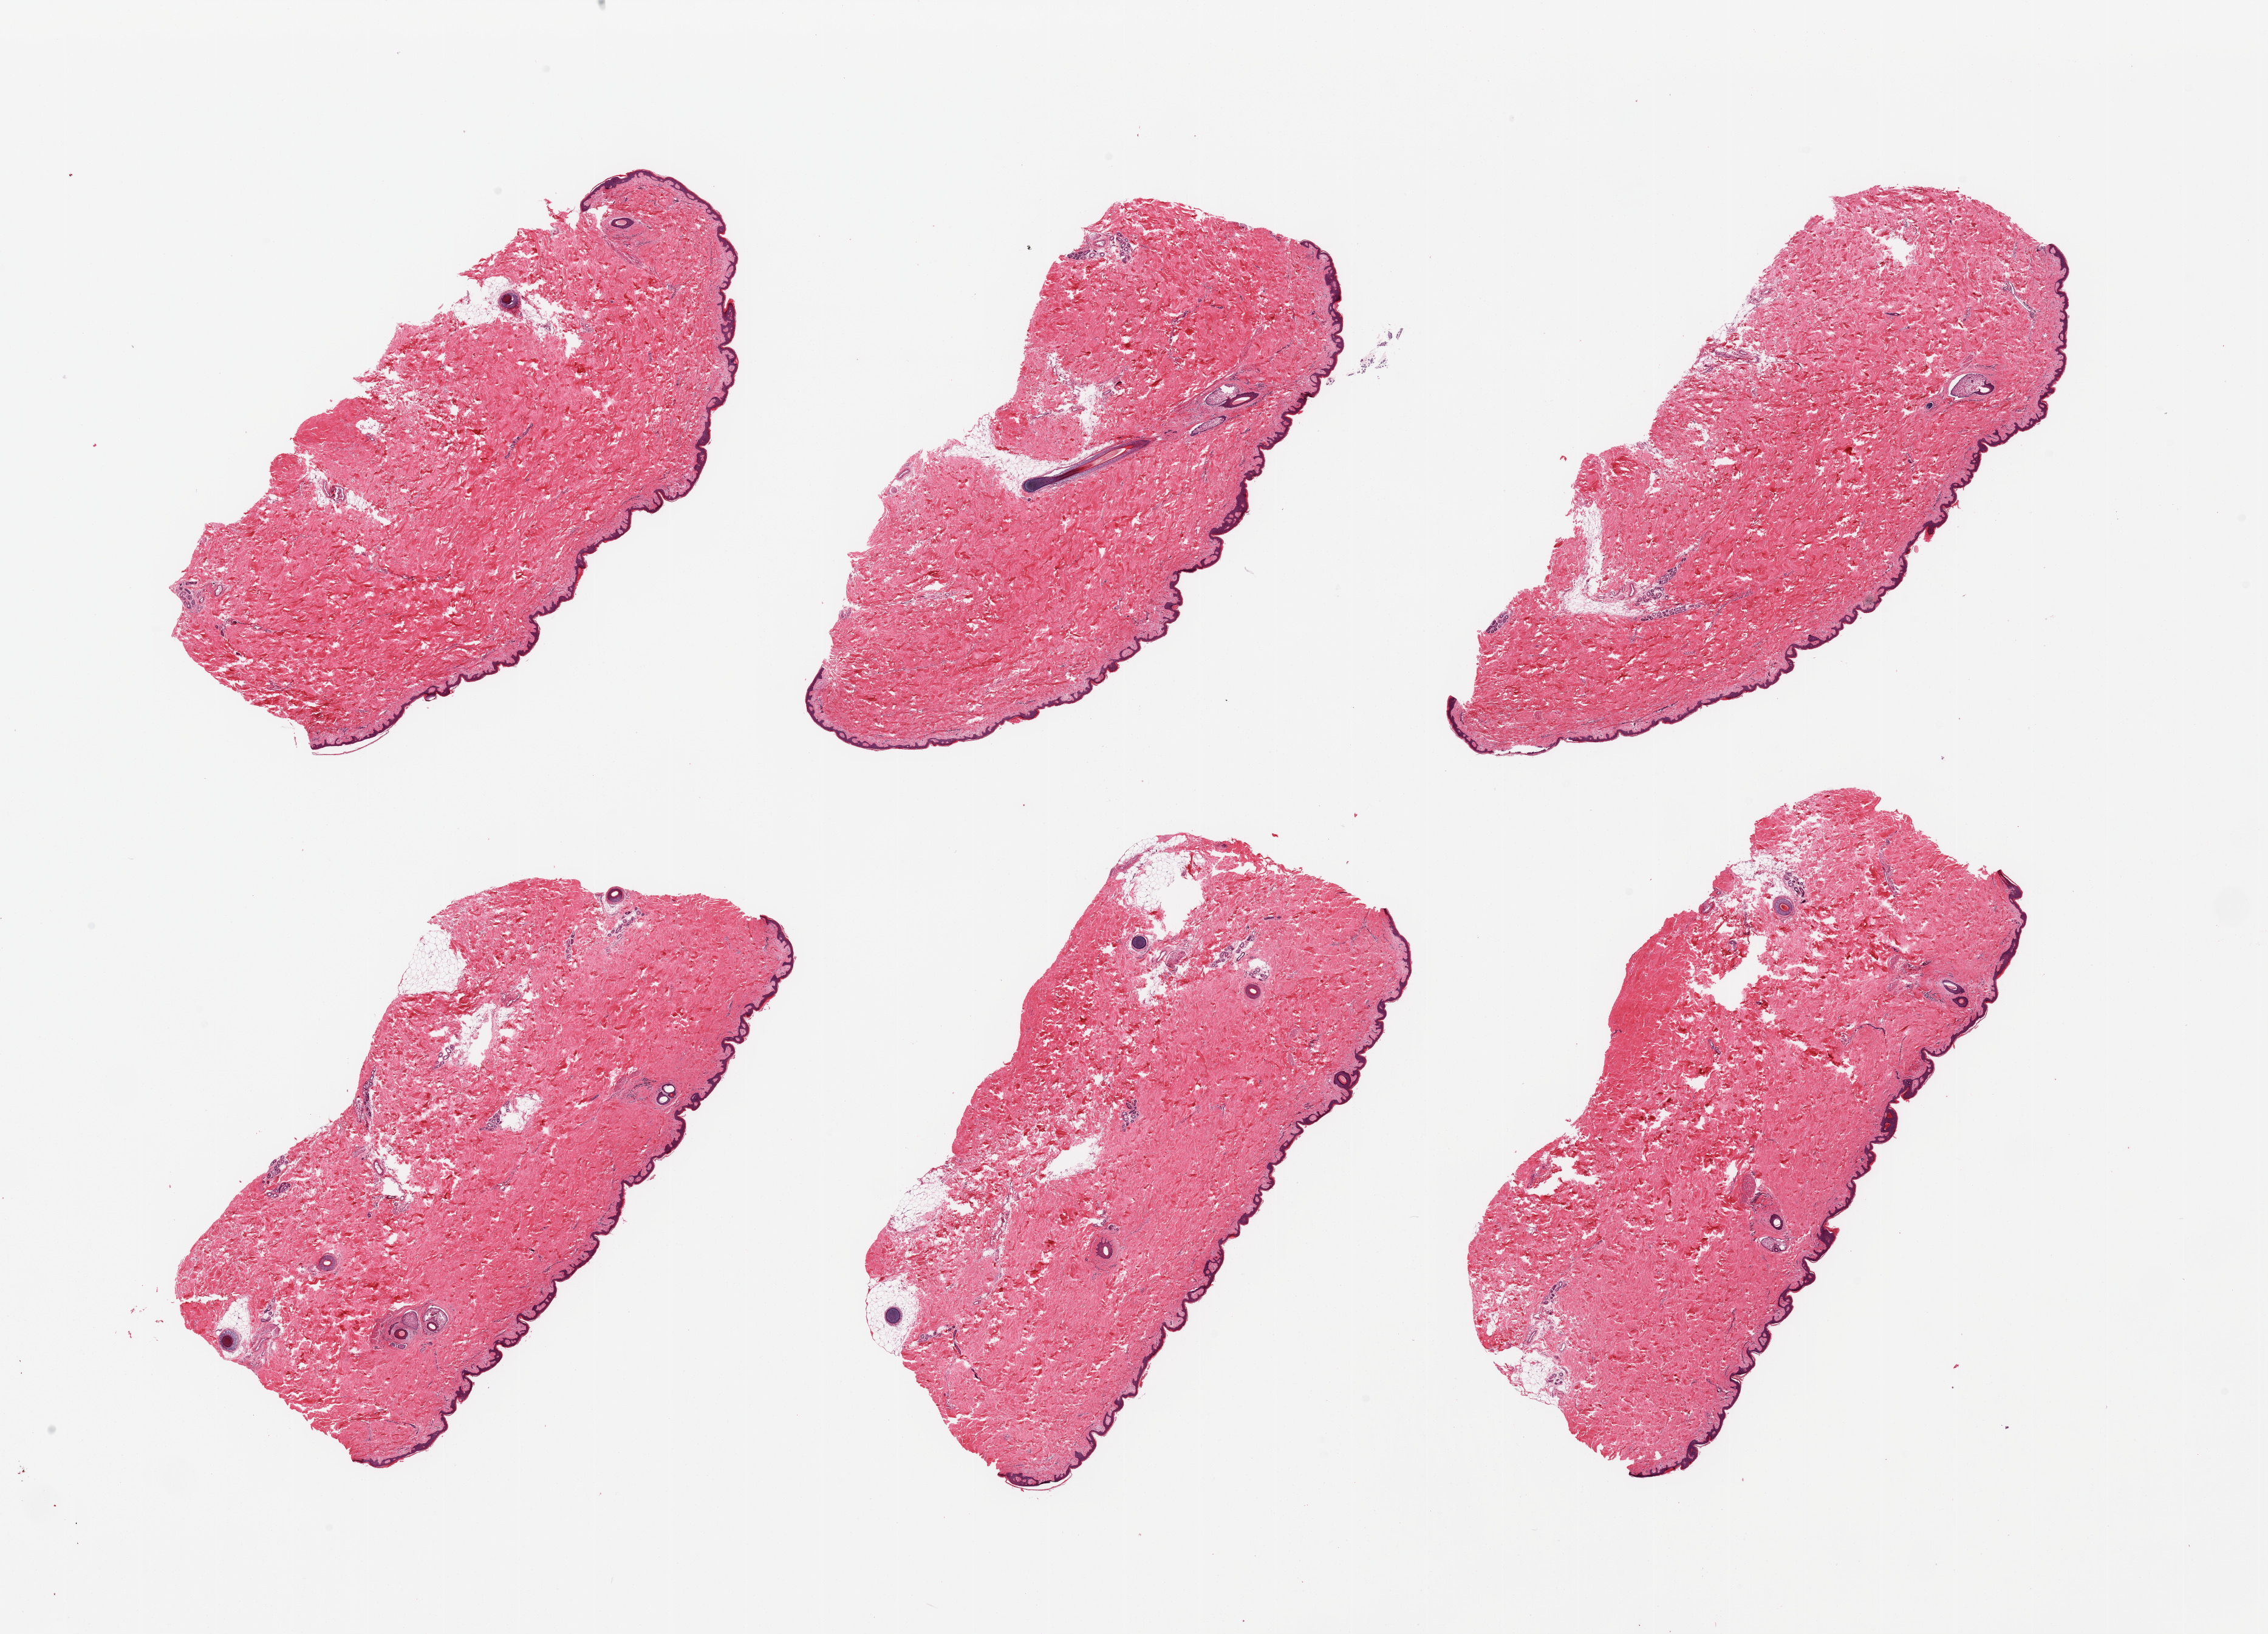
Digitized haematoxylin and eosin-stained section — whole scanned area (about 29.5 x 21.3 mm) shown as a low-resolution overview, PAXgene-fixed paraffin-embedded (PFPE) section, sampled site (target tissue): skin of suprapubic region, tissue donor sample. Male donor.
Pathologist's review note for this sample: 6 pieces, trace dermal fat; squamous epithelium is ~30-35 microns.